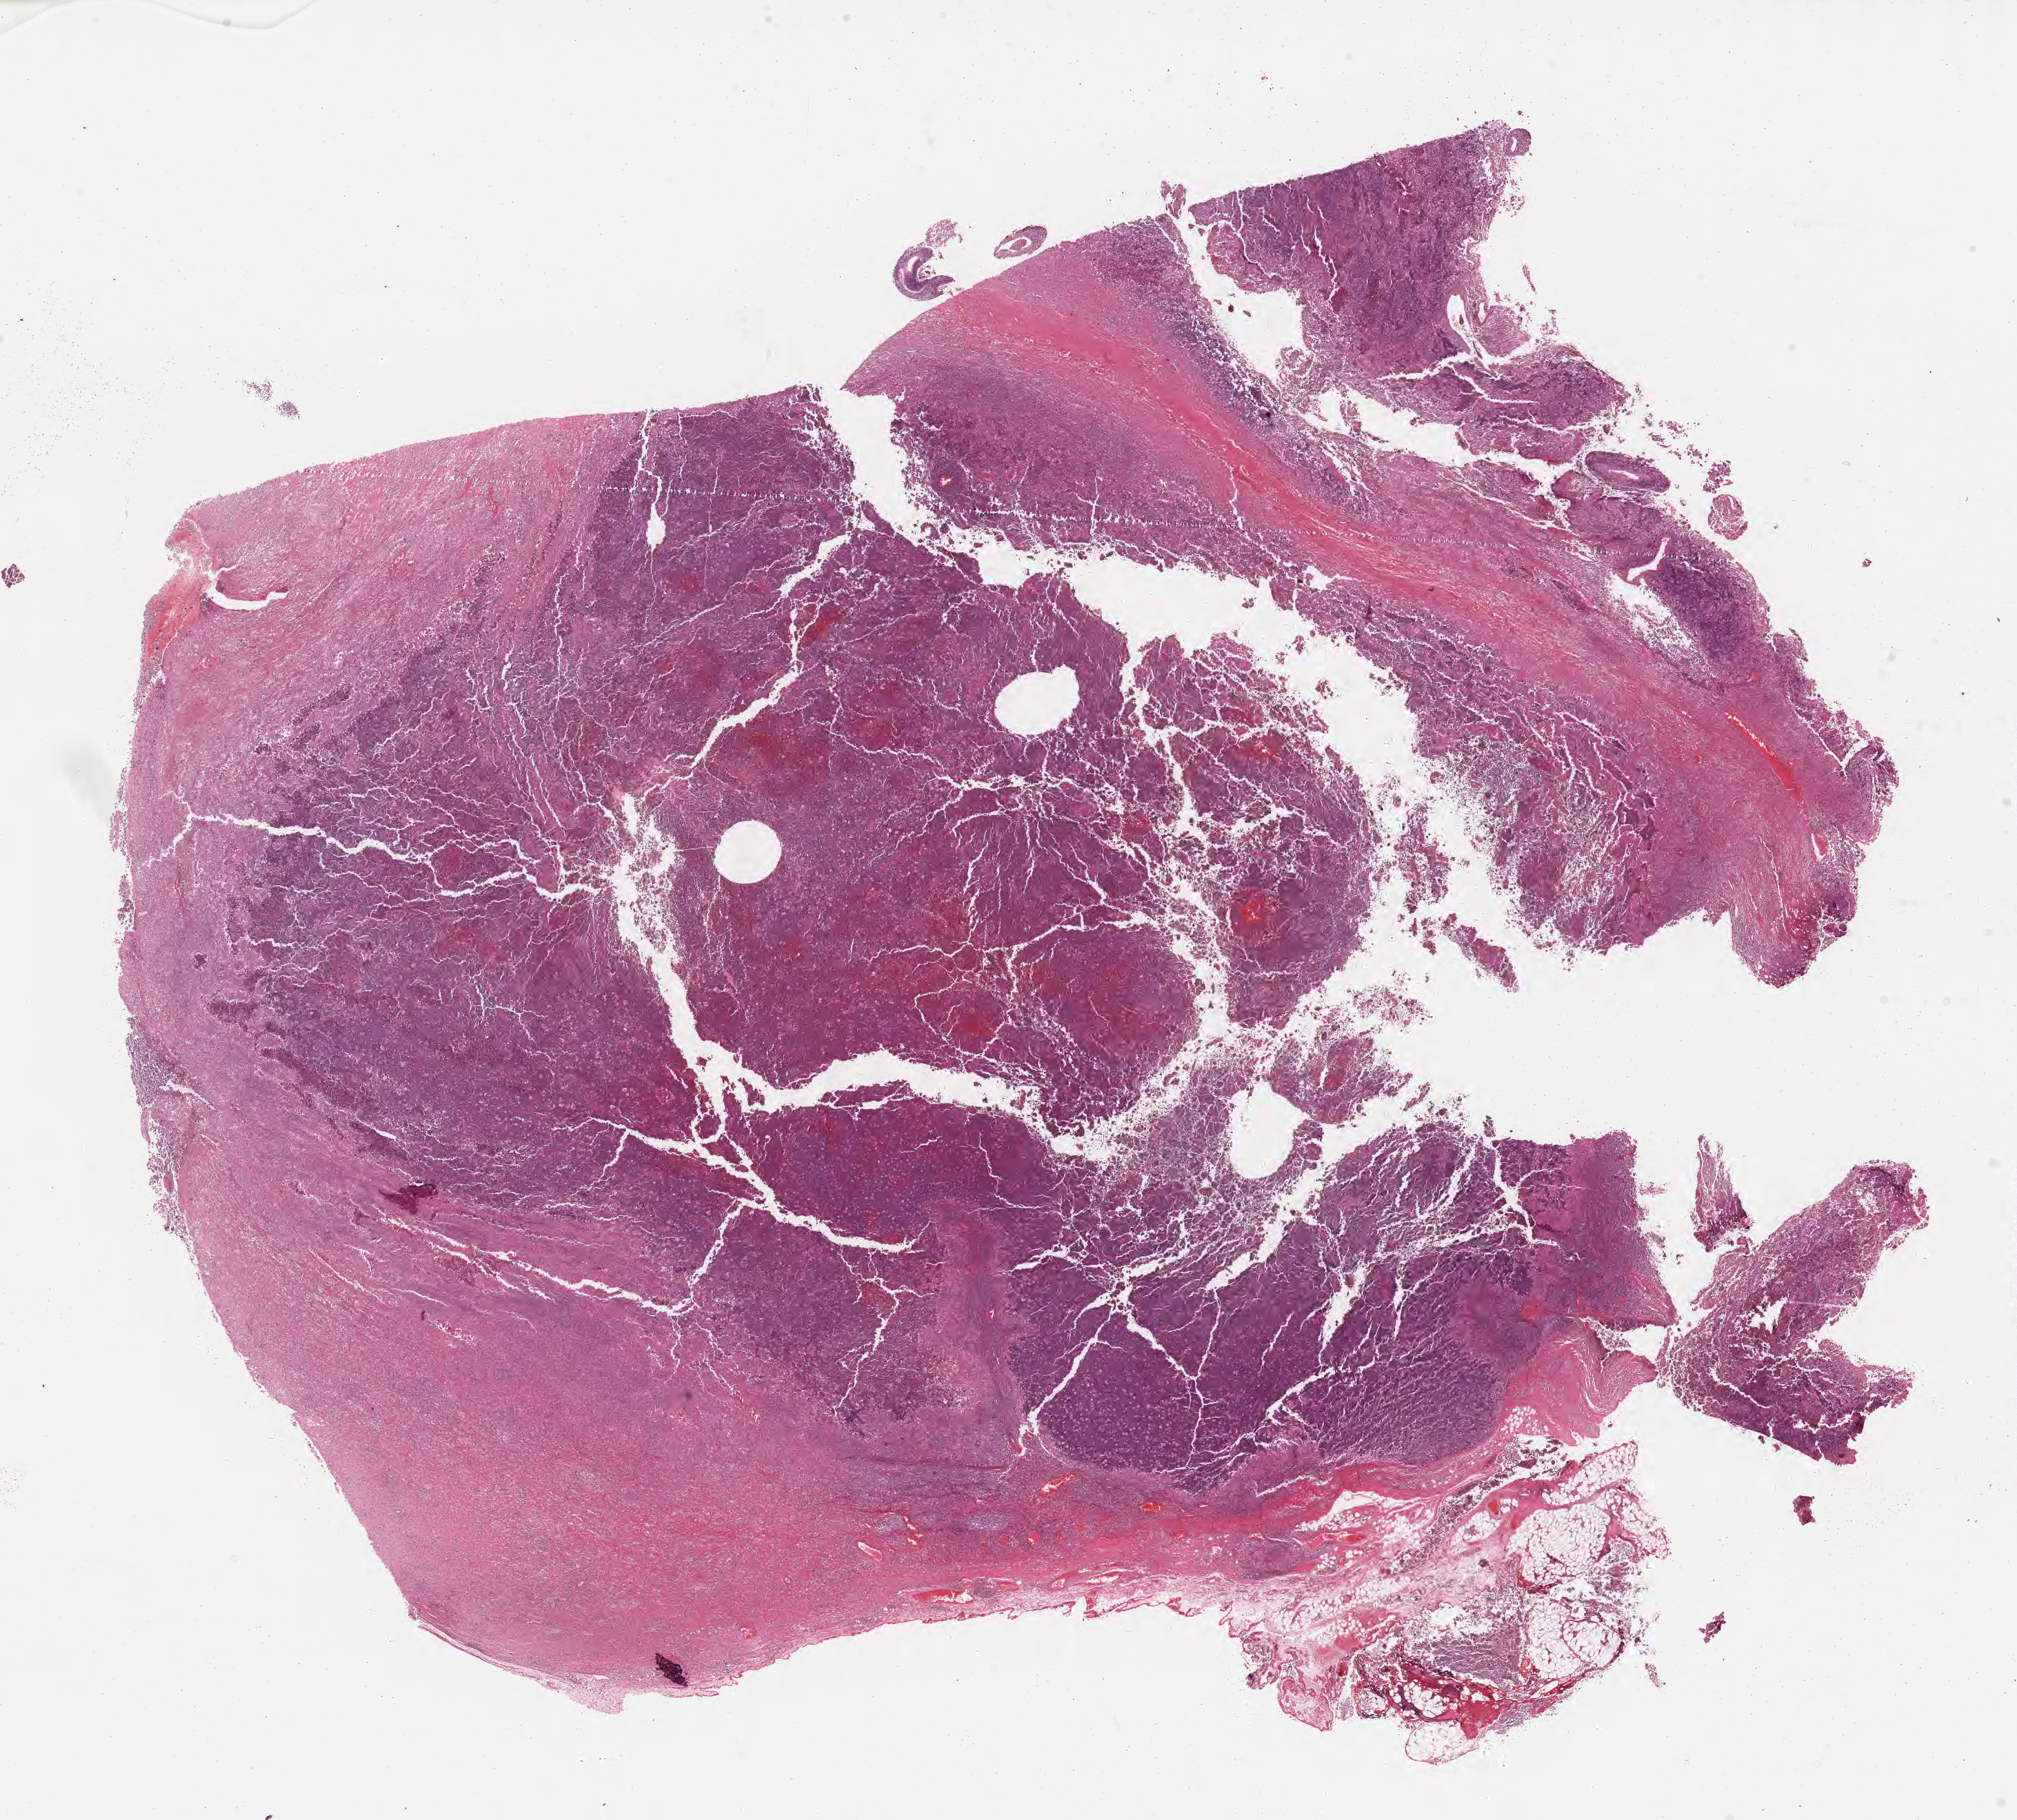
Whole-slide image, H&E stain, shown as a low-resolution overview of the whole scanned area (about 23.6 x 21.3 mm); formalin-fixed, paraffin-embedded (FFPE) tissue; primary tumor. Patient female; age 74 years. Slide review estimates, as recorded: tumor cells 70%, tumor nuclei 80%, stromal cells 20%, necrosis 5%, normal cells 5%. Infiltration values recorded for this section: lymphocyte infiltration 60%, monocyte infiltration 20%, neutrophil infiltration 5%.
Diagnosis: Burkitt lymphoma, NOS. Ann Arbor stage (patient): Stage III.